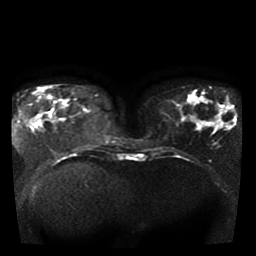
Breast MRI, one axial slice; position 14 of 41 along the scan axis; diffusion-weighted series; image 2 of 4 stored at this slice position (different b-values; order by instance number); 1.5 T; 5 mm slice thickness; 256 × 256 image matrix, field of view 330 × 330 mm. Female patient.
Annotated regions visible in this slice (manually delineated by an expert):
- tumour on diffusion-weighted imaging: bounding box <23,114,39,124> (left, top, right, bottom; pixels)